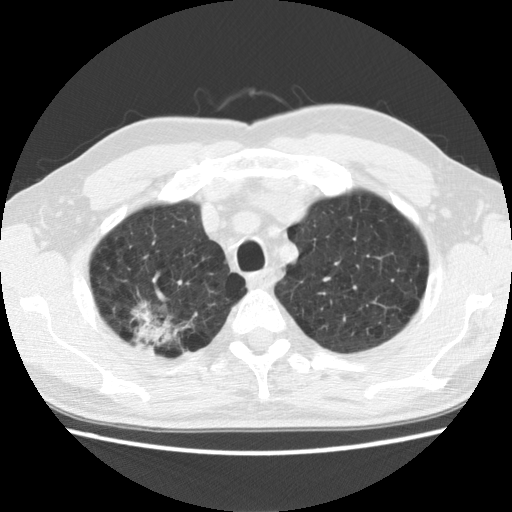
Axial slice from a low-dose chest CT screening exam, baseline screening round, lung window (W 1500 / L -600 HU), 2.5 mm slice thickness, 120 kVp, slice 28 of 142 in the series. Male, age 64 years at enrolment. Former smoker at enrolment.
Expert-annotated lung lesion, box from (x=110, y=290) to (x=198, y=363) px. Screening reader's record for this exam (one nodule recorded; not confirmed to be the boxed lesion): non-calcified nodule or mass ≥4 mm, right upper lobe, 39 × 31 mm, spiculated (stellate) margins, mixed attenuation. Later outcome: lung cancer diagnosed 74 days after this screen — adenocarcinoma, NOS, right upper lobe, moderately differentiated (G2), stage IB (AJCC 6th edition), 40 mm at pathology.